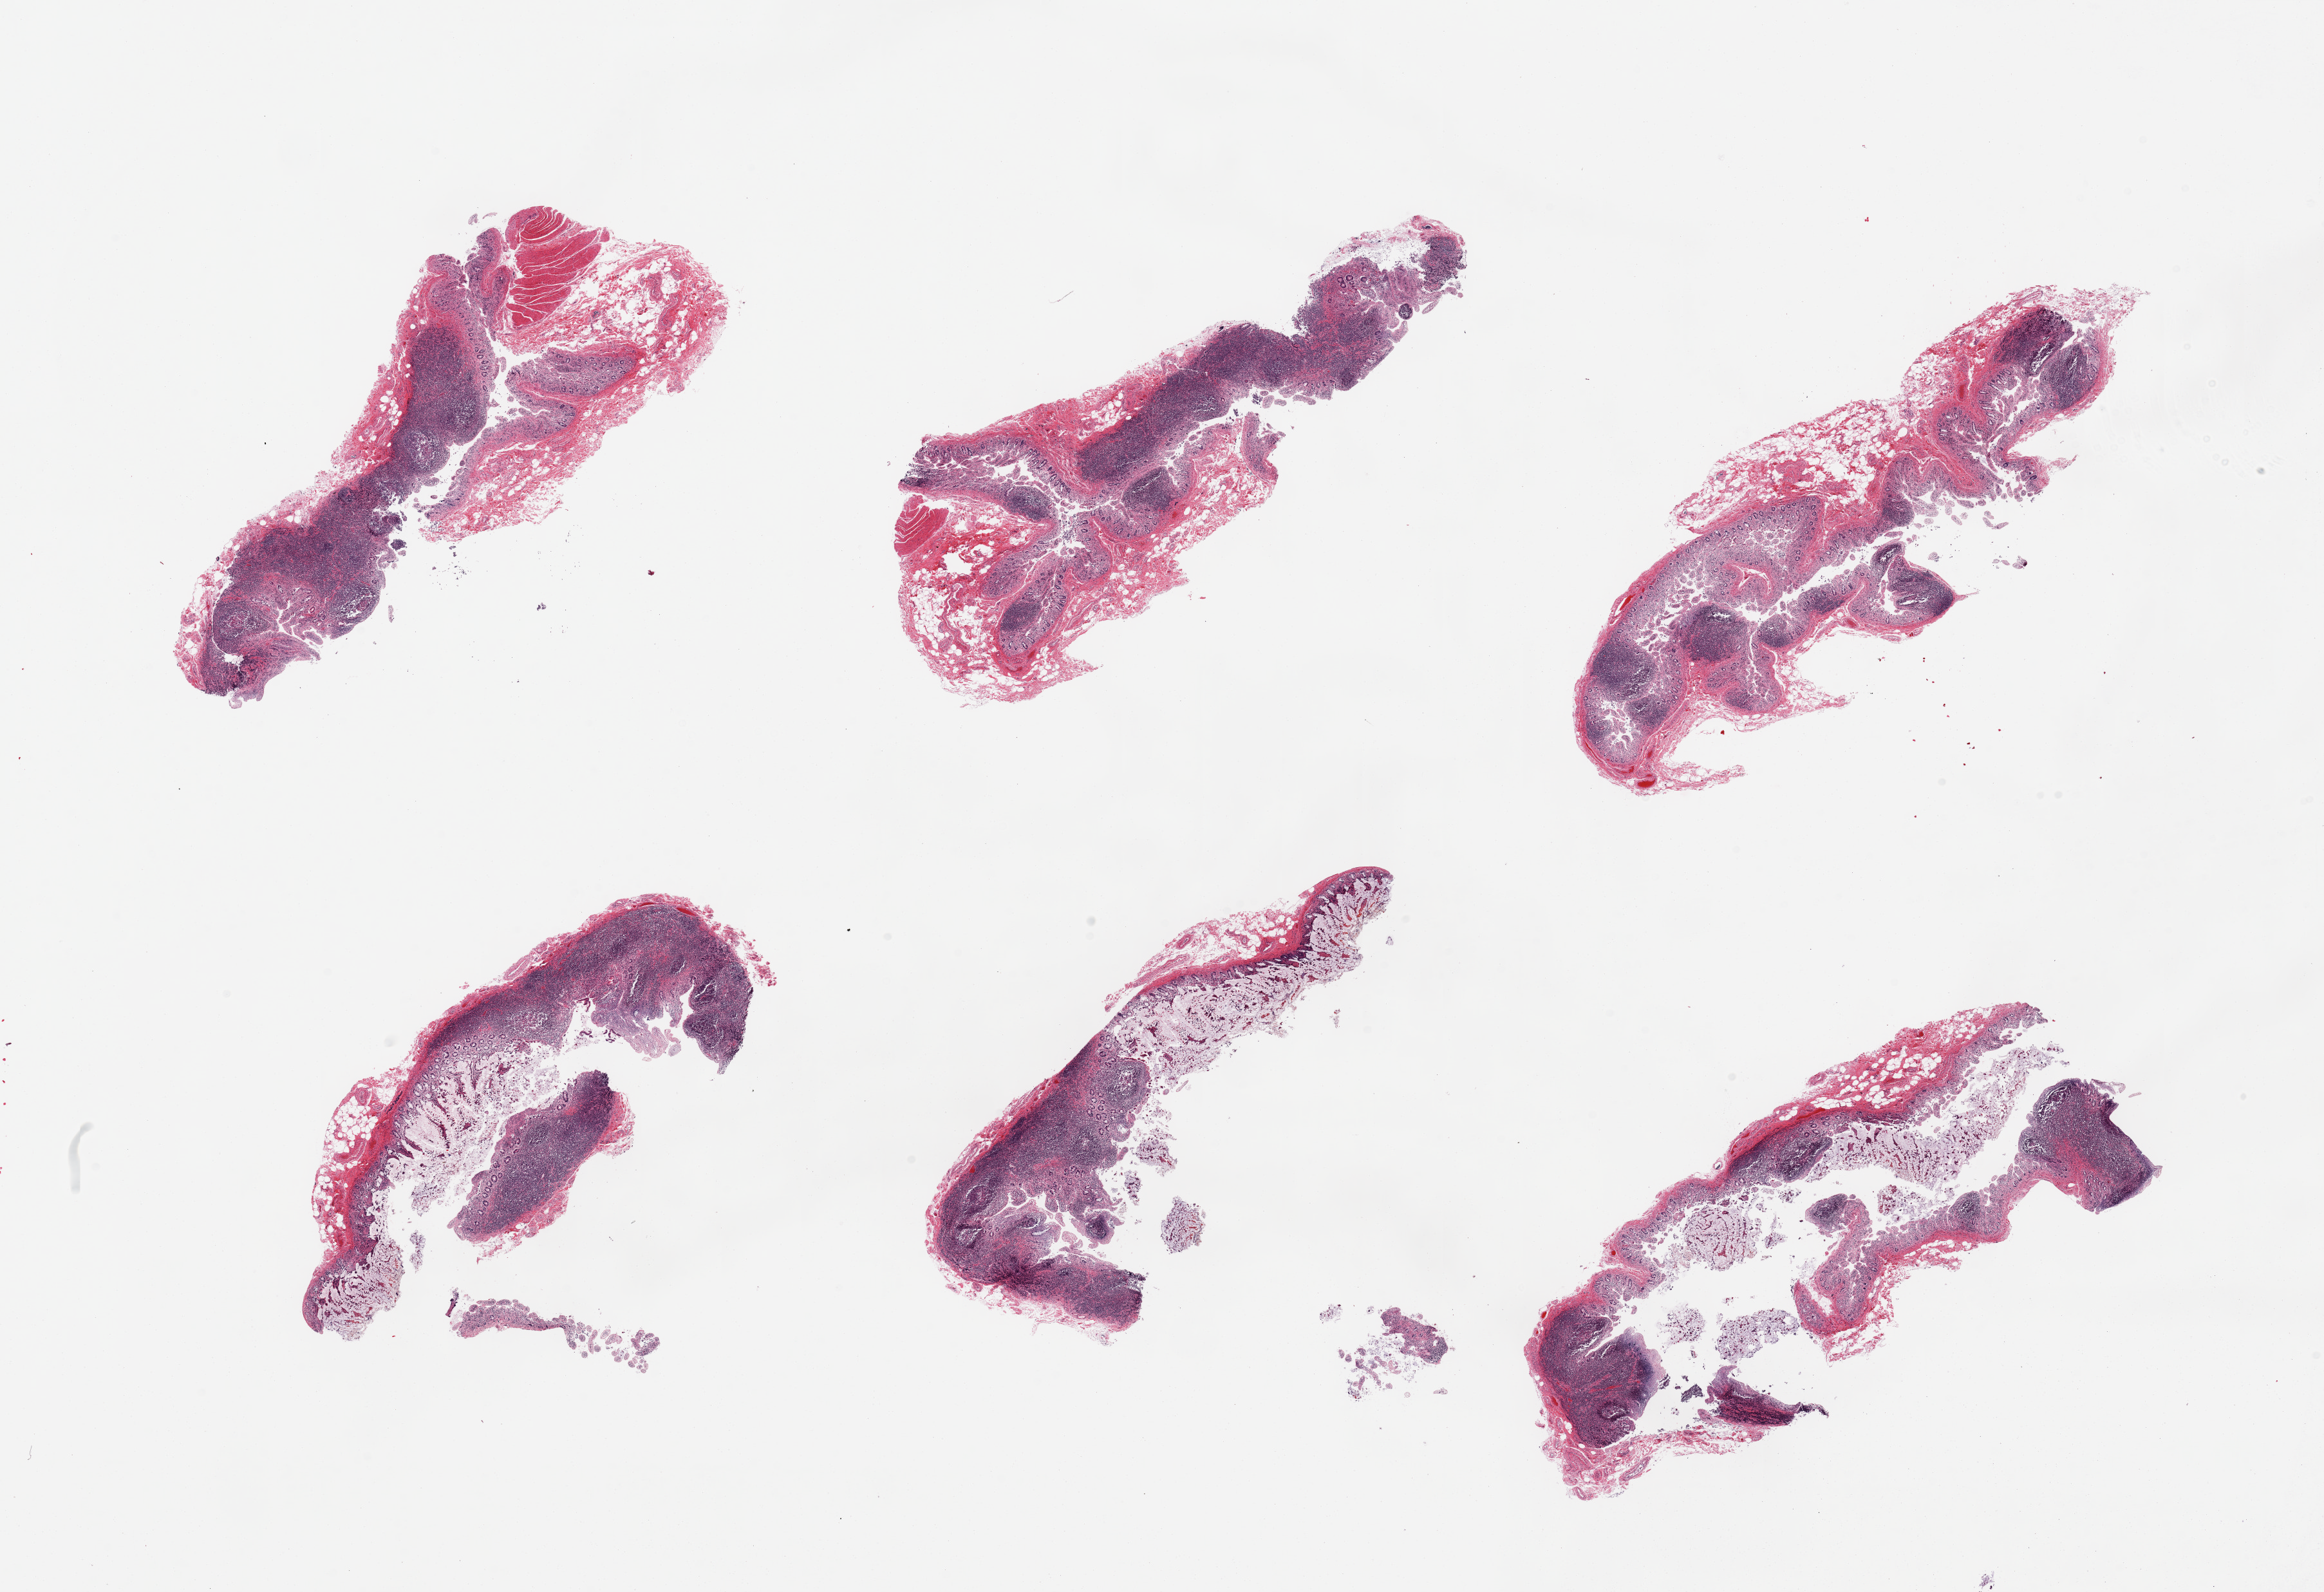
Digitized hematoxylin and eosin (H&E)-stained section — shown as a low-resolution overview of the whole scanned area (about 28.5 x 19.6 mm), PAXgene-fixed paraffin-embedded (PFPE) section, sampled site (target tissue): ileum, tissue donor sample. Donor: male.
Review note (as recorded): 6 pieces, mucosal epithelium totally autolyzed; ~50% tissue is residual lymphoid aggregates, fairly well preserved.